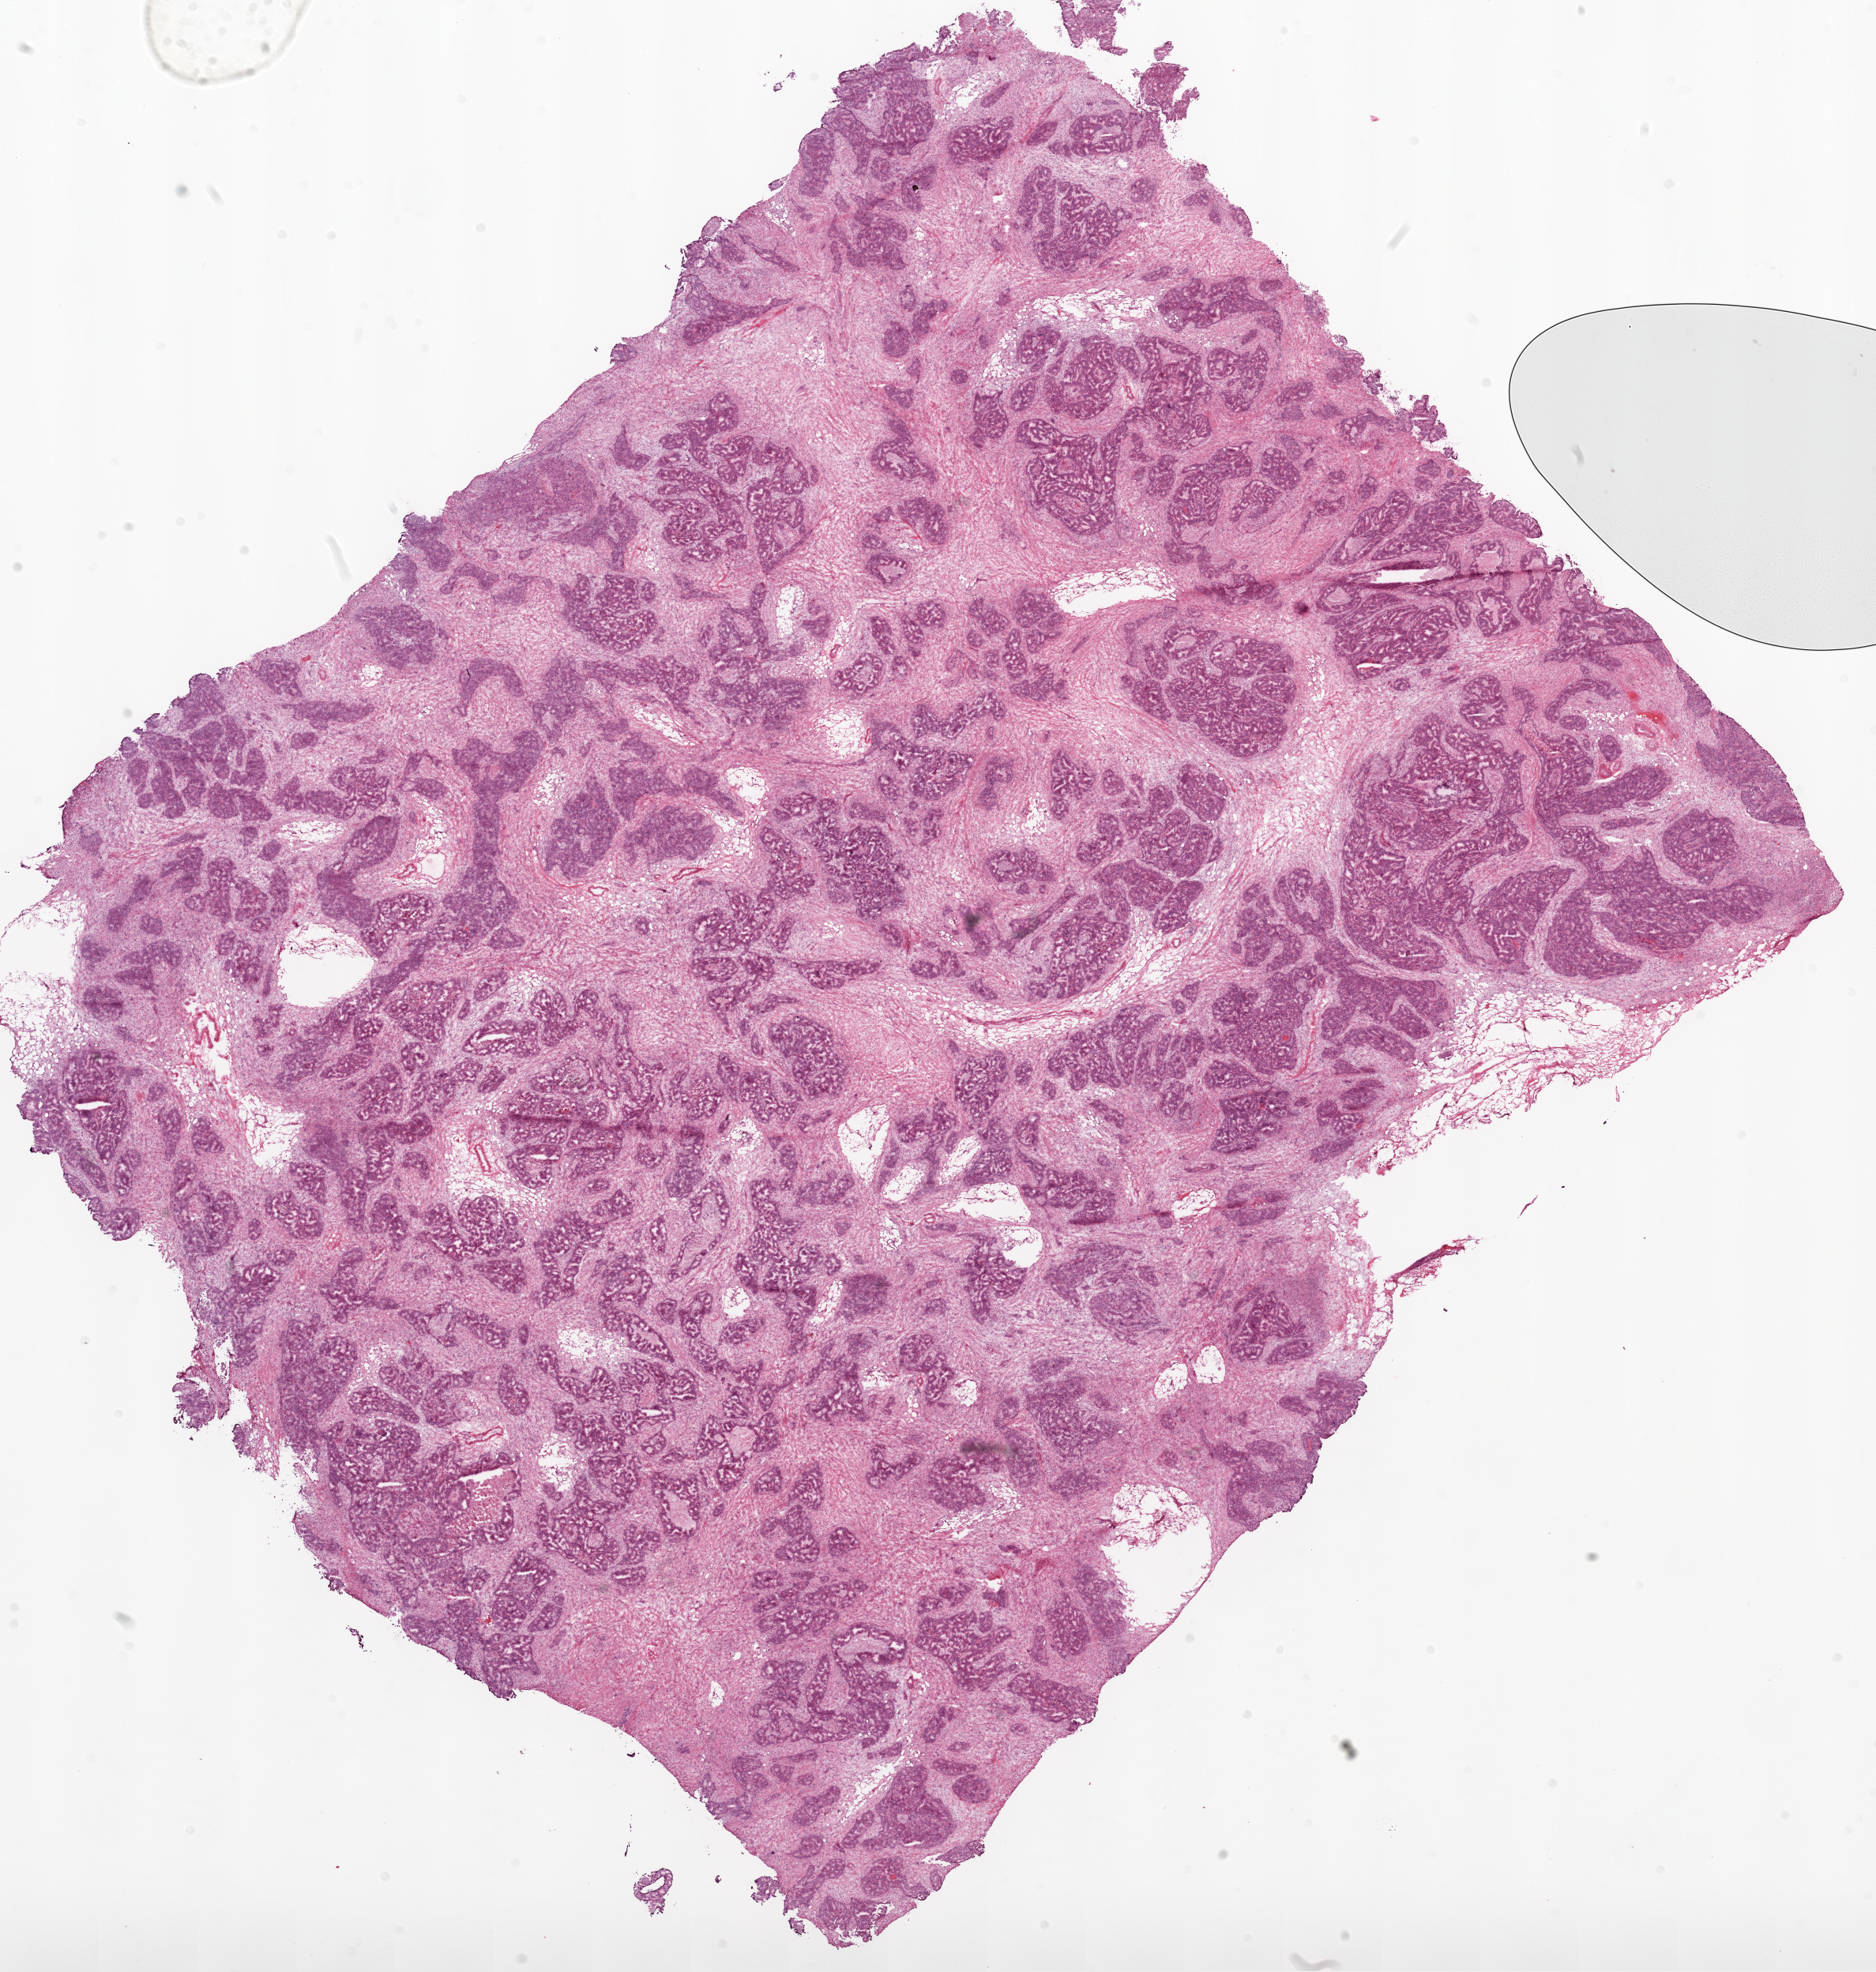
Whole-slide histology image, Hematoxylin and eosin (H&E) stained — a low-resolution overview of the entire scanned area, about 19.1 x 20.0 mm (from a 20x scan), frozen section from the top of the tissue portion, sample: primary tumour, ovary. Female patient; age at initial diagnosis 71 years. Pathologist review of this section (percent, as recorded): tumour cells 80%, tumour nuclei 85%.
Histologic diagnosis: Serous cystadenocarcinoma, NOS.